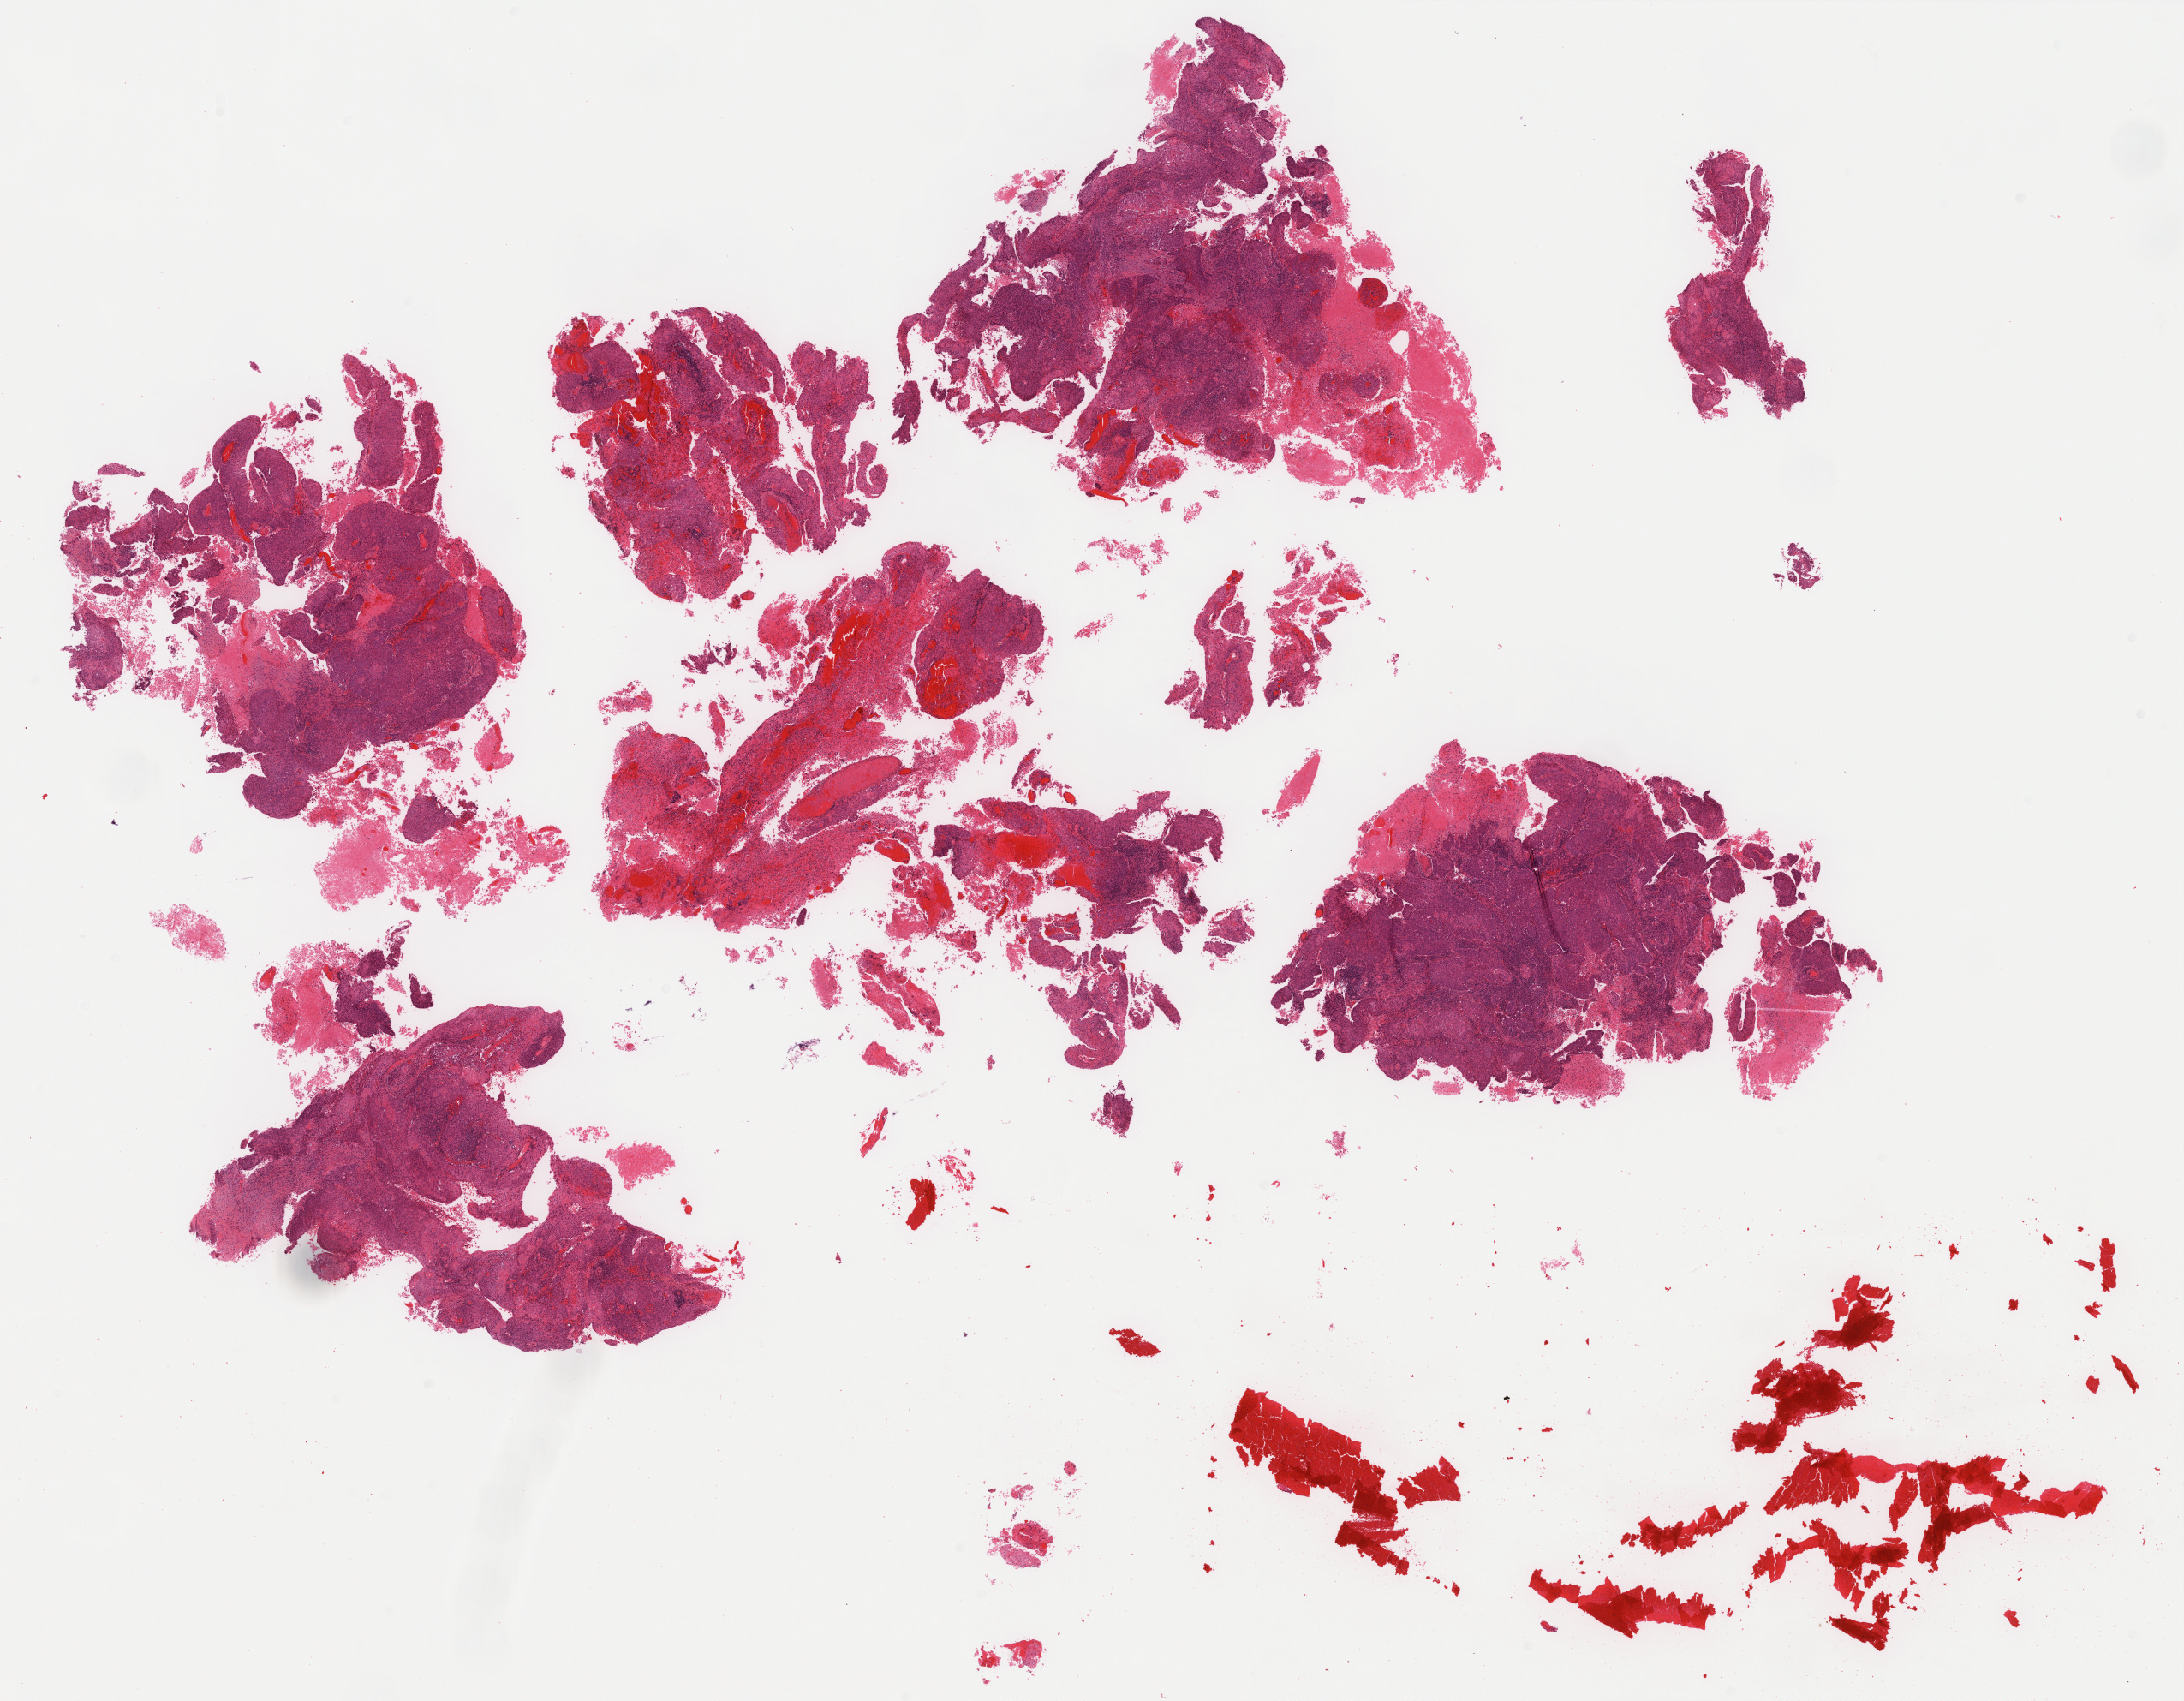
H&E-stained whole-slide image, low-resolution overview of the scanned area, about 20.4 x 15.9 mm (from a 40x scan); formalin-fixed paraffin-embedded (FFPE) diagnostic section; sample: primary tumour, cervix. Female patient; age at initial diagnosis 65 years. Histologic grade: G2 (moderately differentiated).
Pathologic diagnosis: Squamous cell carcinoma, keratinizing, NOS (cervix uteri). FIGO stage: IIIB.